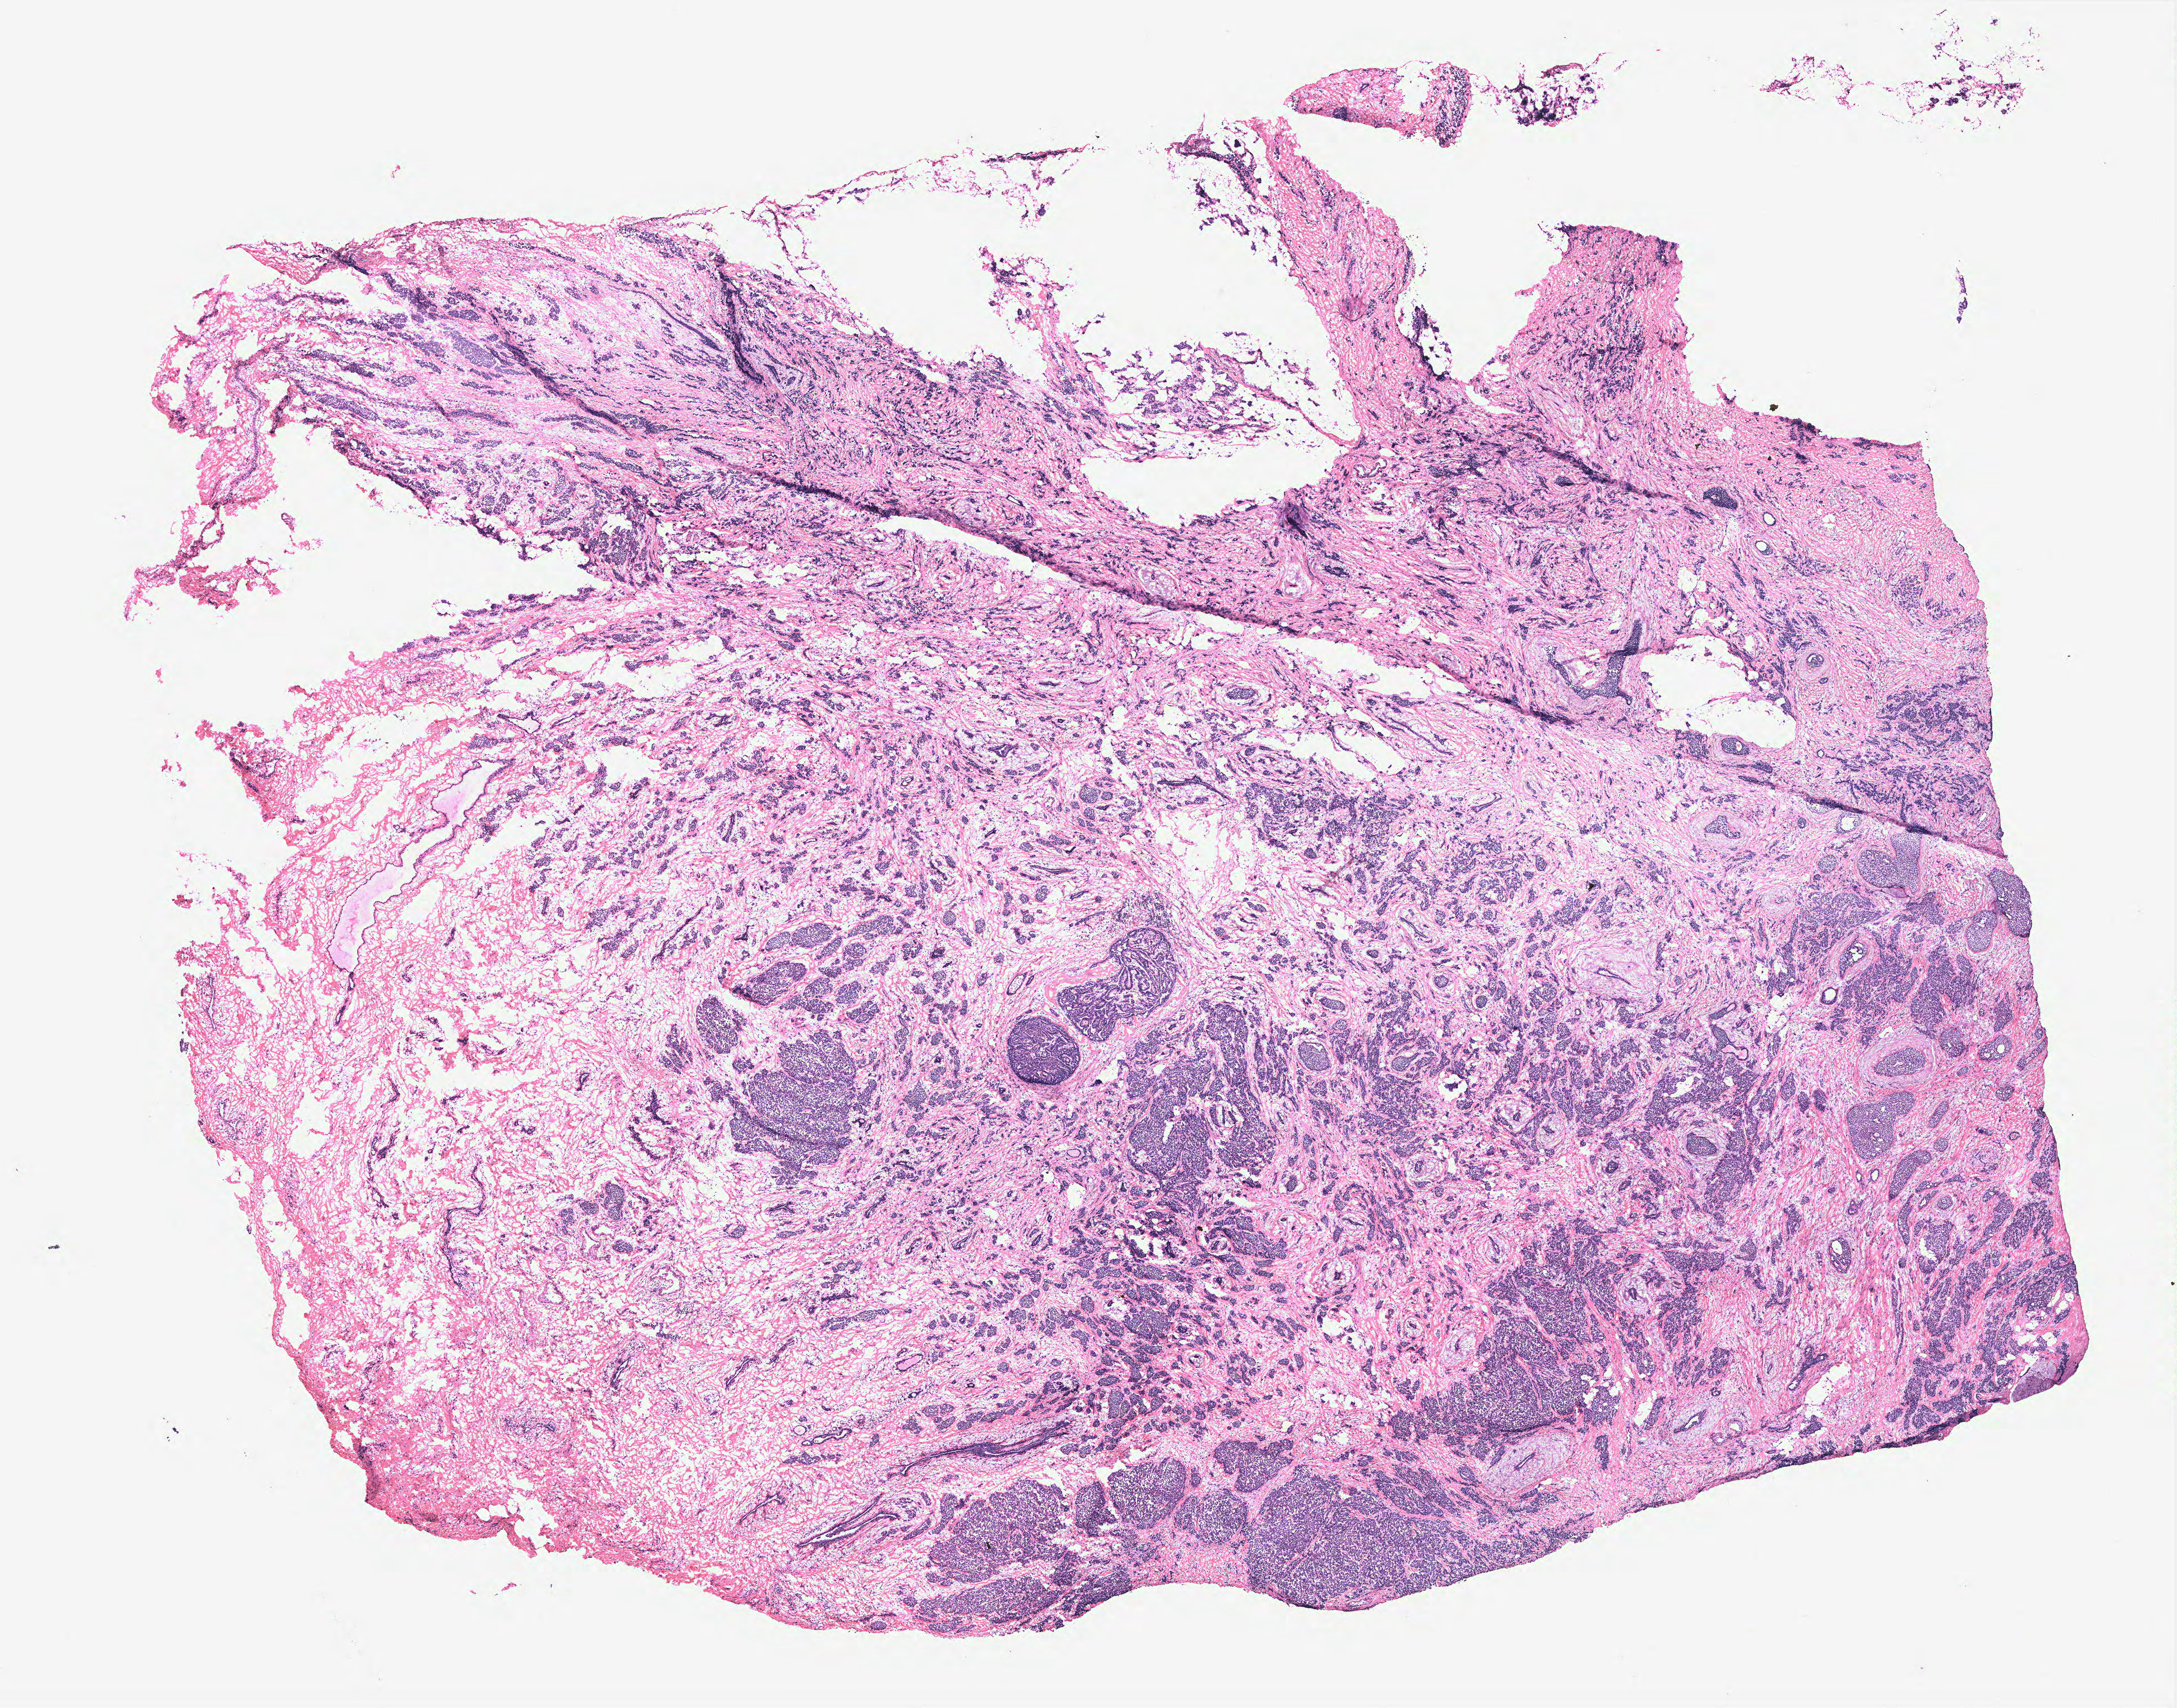
Digitized Hematoxylin and eosin (H&E) stained tissue section (whole slide), low-resolution overview of the scanned area, about 15.6 x 12.2 mm (acquisition: 40x scan); breast, tissue type not recorded. Patient: female, age 67 years.
- patient diagnosis: Infiltrating duct carcinoma, NOS